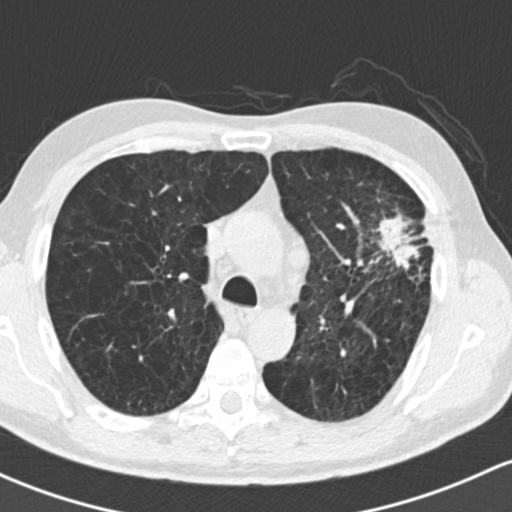
Low-dose screening chest CT, one axial slice. Position 108 of 162 along the scan axis. 120 kVp. Lung window (W 1500 / L -600 HU). 2 mm slice thickness. 512 × 512 image matrix, field of view 318 × 318 mm.
Annotated regions visible in this slice (outlined manually by an expert reader):
- lesion 1 (tumor, upper lobe of left lung): box from (x=376, y=213) to (x=420, y=270) px